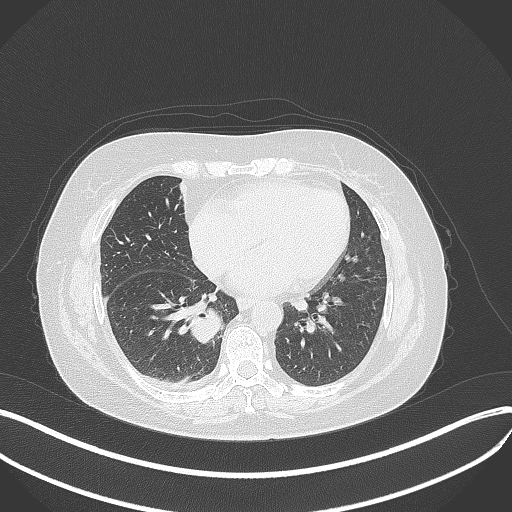
Chest CT, one axial slice; slice 140 of 381 in the series (ordered by position); reconstruction kernel B70f; lung window (W 1500 / L -600 HU); 512 × 512 image matrix, field of view 400 × 400 mm. Female patient, age 56 years. Case-level facts recorded for this patient, not image findings: clinical TNM (as recorded): T2b N1 M0.
Outlined on this slice (rectangle marked by the reading radiologist):
- lung tumour (recorded histology: small cell carcinoma): bounding box [x1, y1, x2, y2] px = [189, 307, 230, 343]